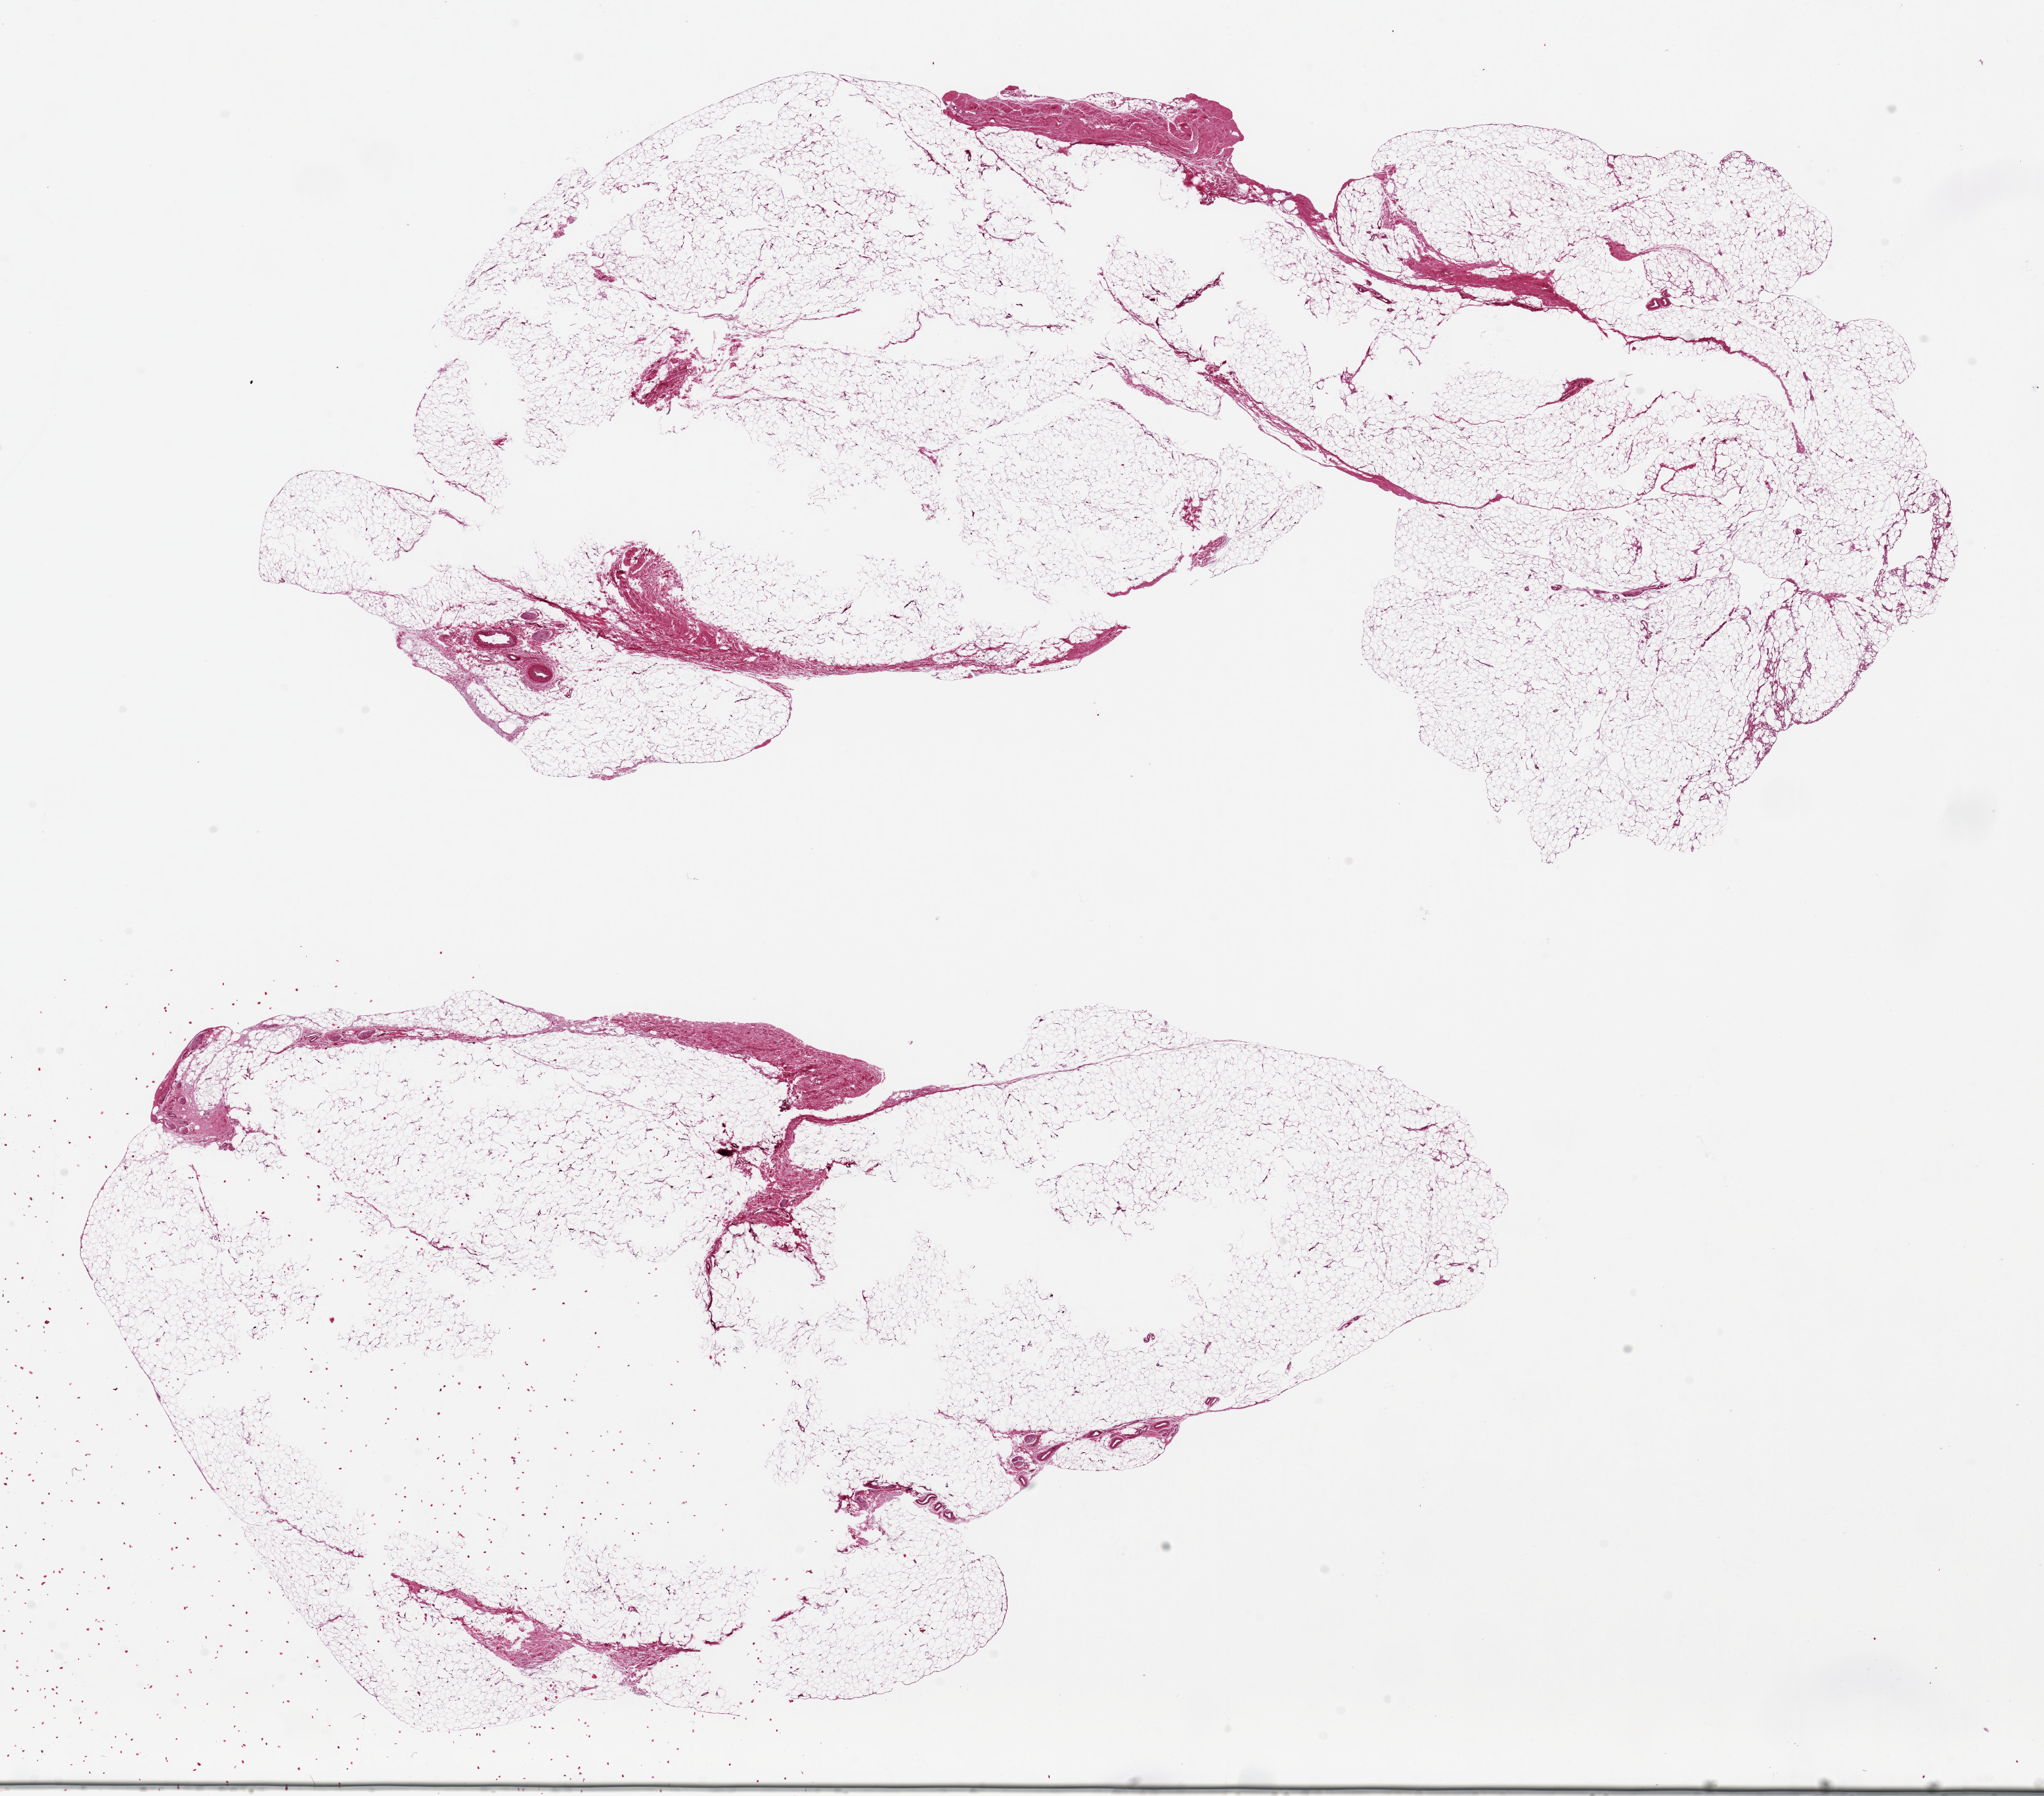
Hematoxylin and eosin (H&E) whole-slide image — whole scanned area (about 24.6 x 21.6 mm) shown as a low-resolution overview; PAXgene-fixed, paraffin-embedded tissue; section of adipose tissue (target tissue); donor tissue sample. Donor: female.
Reviewer comment on this tissue sample: 2 pieces, ~15x9mm.